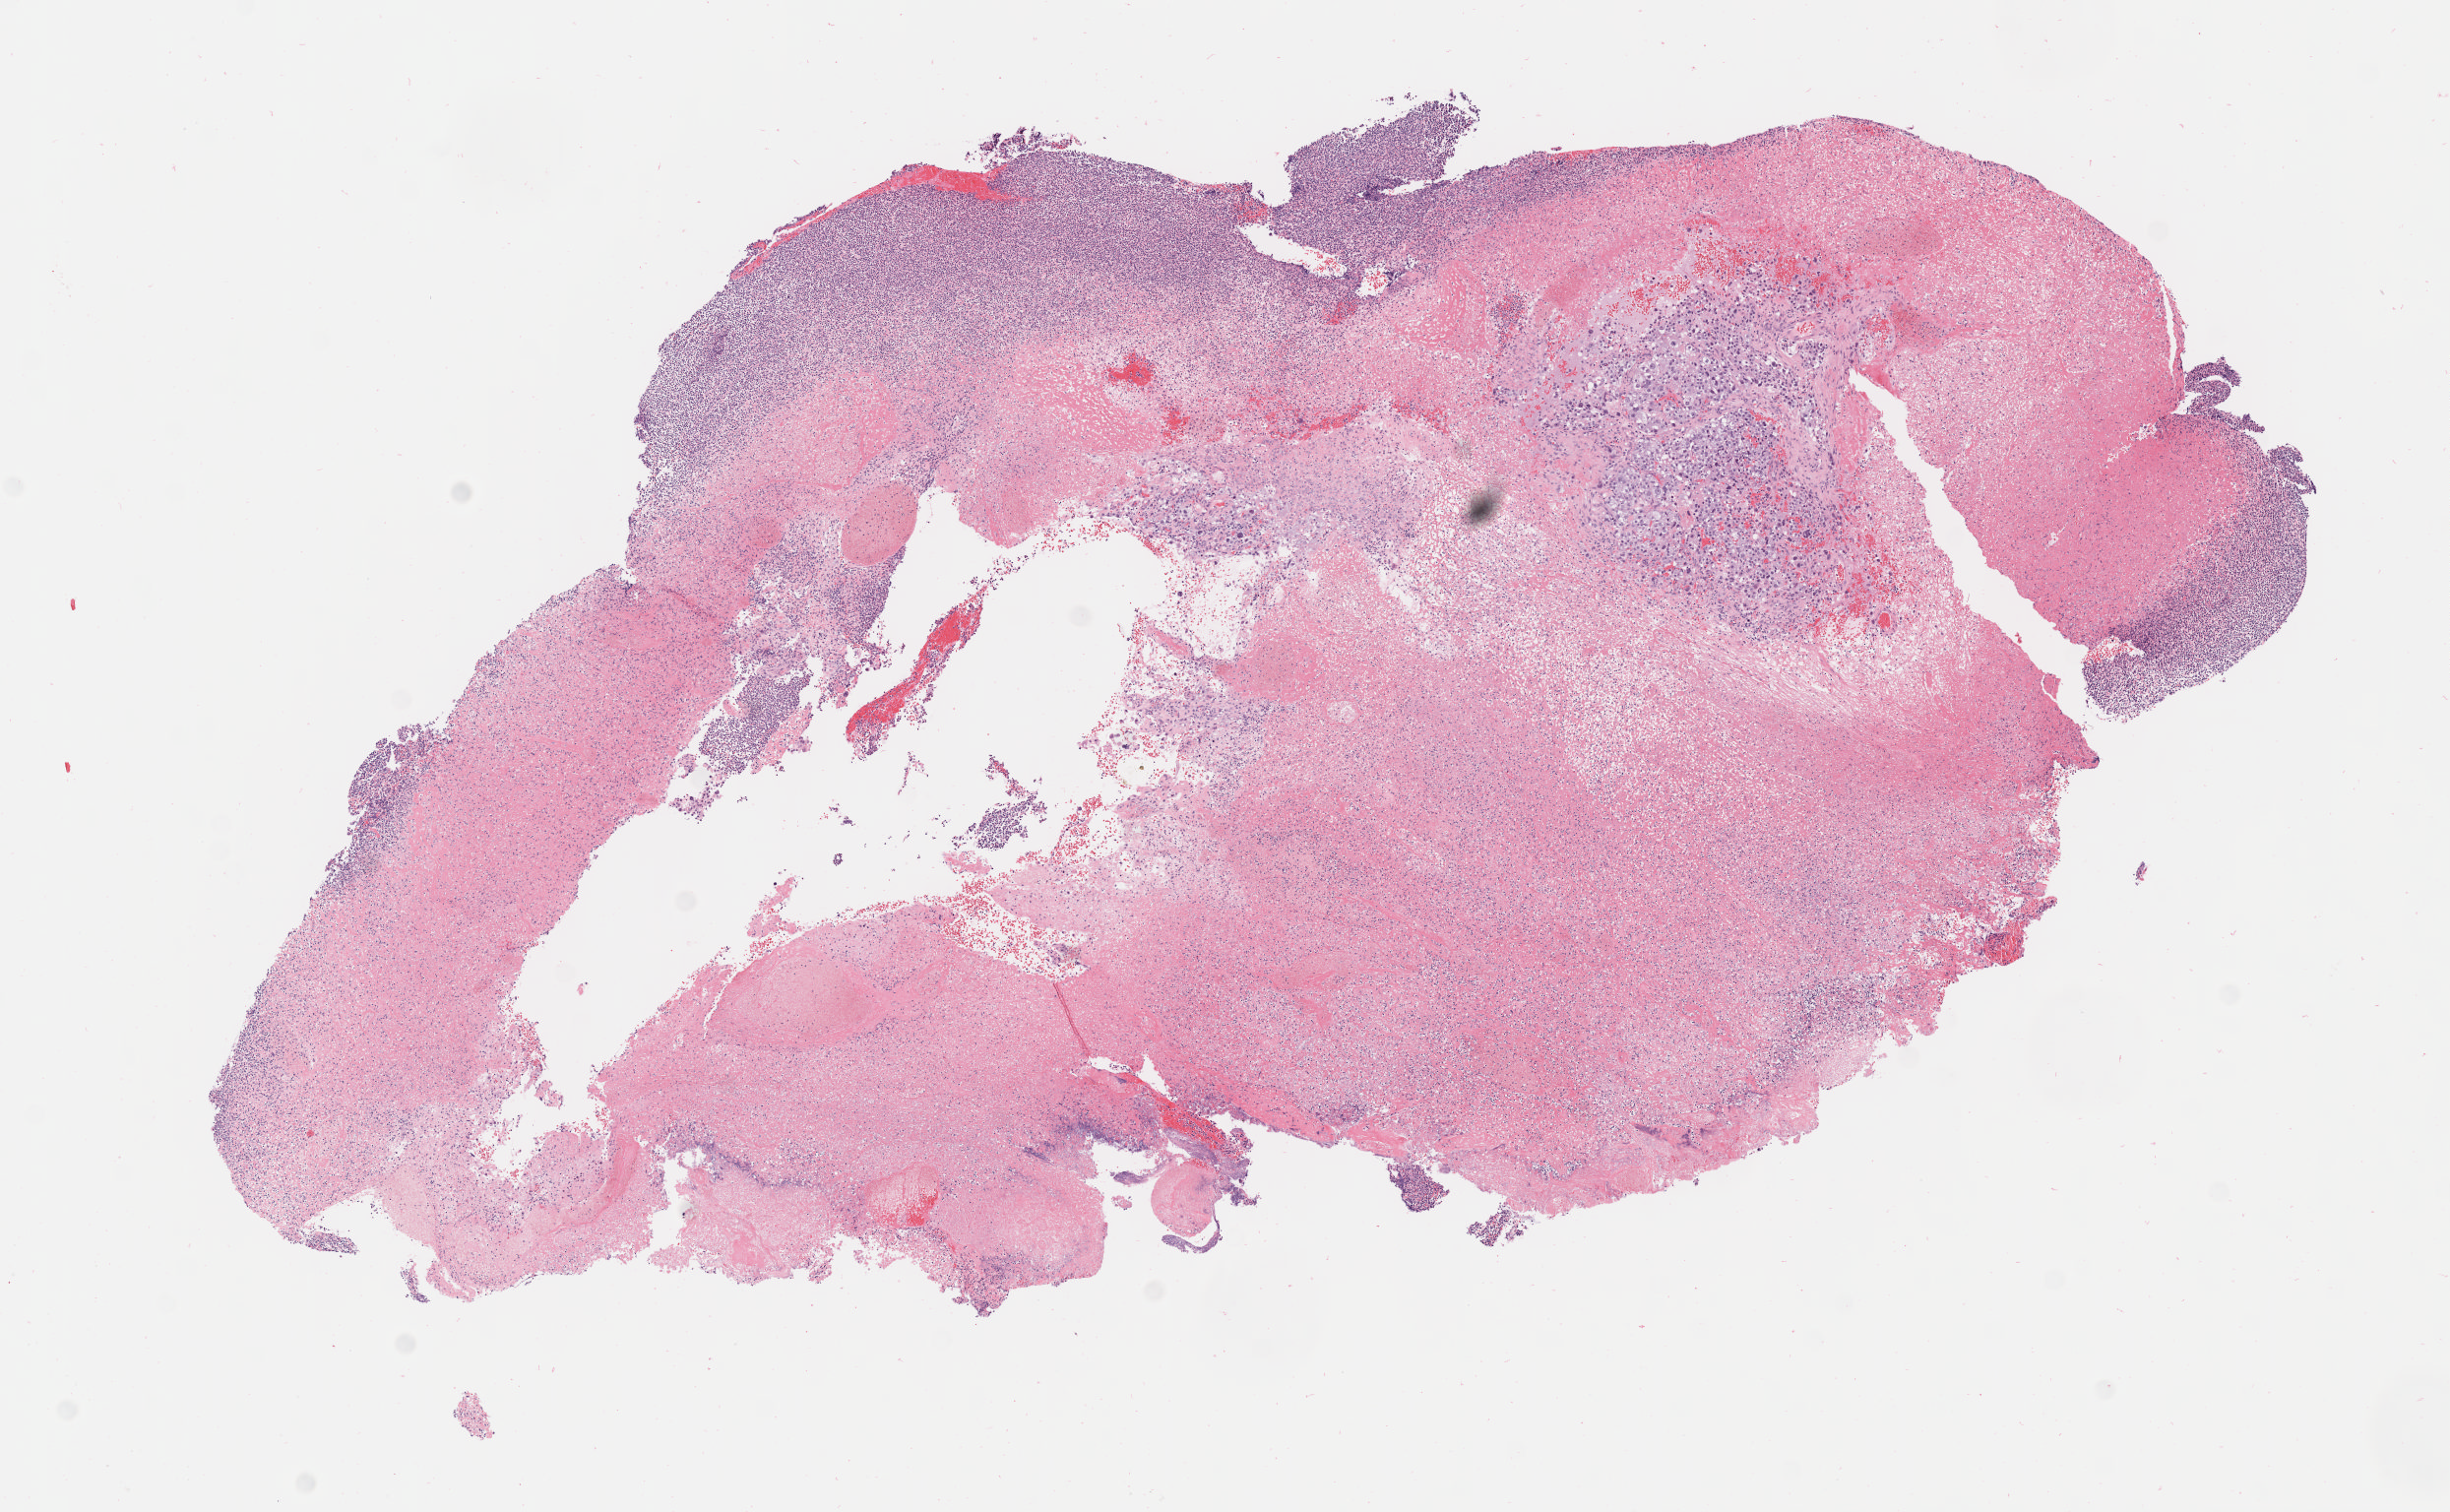
Haematoxylin and eosin whole-slide image, low-resolution overview of the scanned area, about 10.1 x 6.2 mm; specimen: tumor tissue; anatomic site: cervix. Patient: female, aged 62.
* histologic diagnosis: Squamous cell carcinoma, large cell, nonkeratinizing, NOS